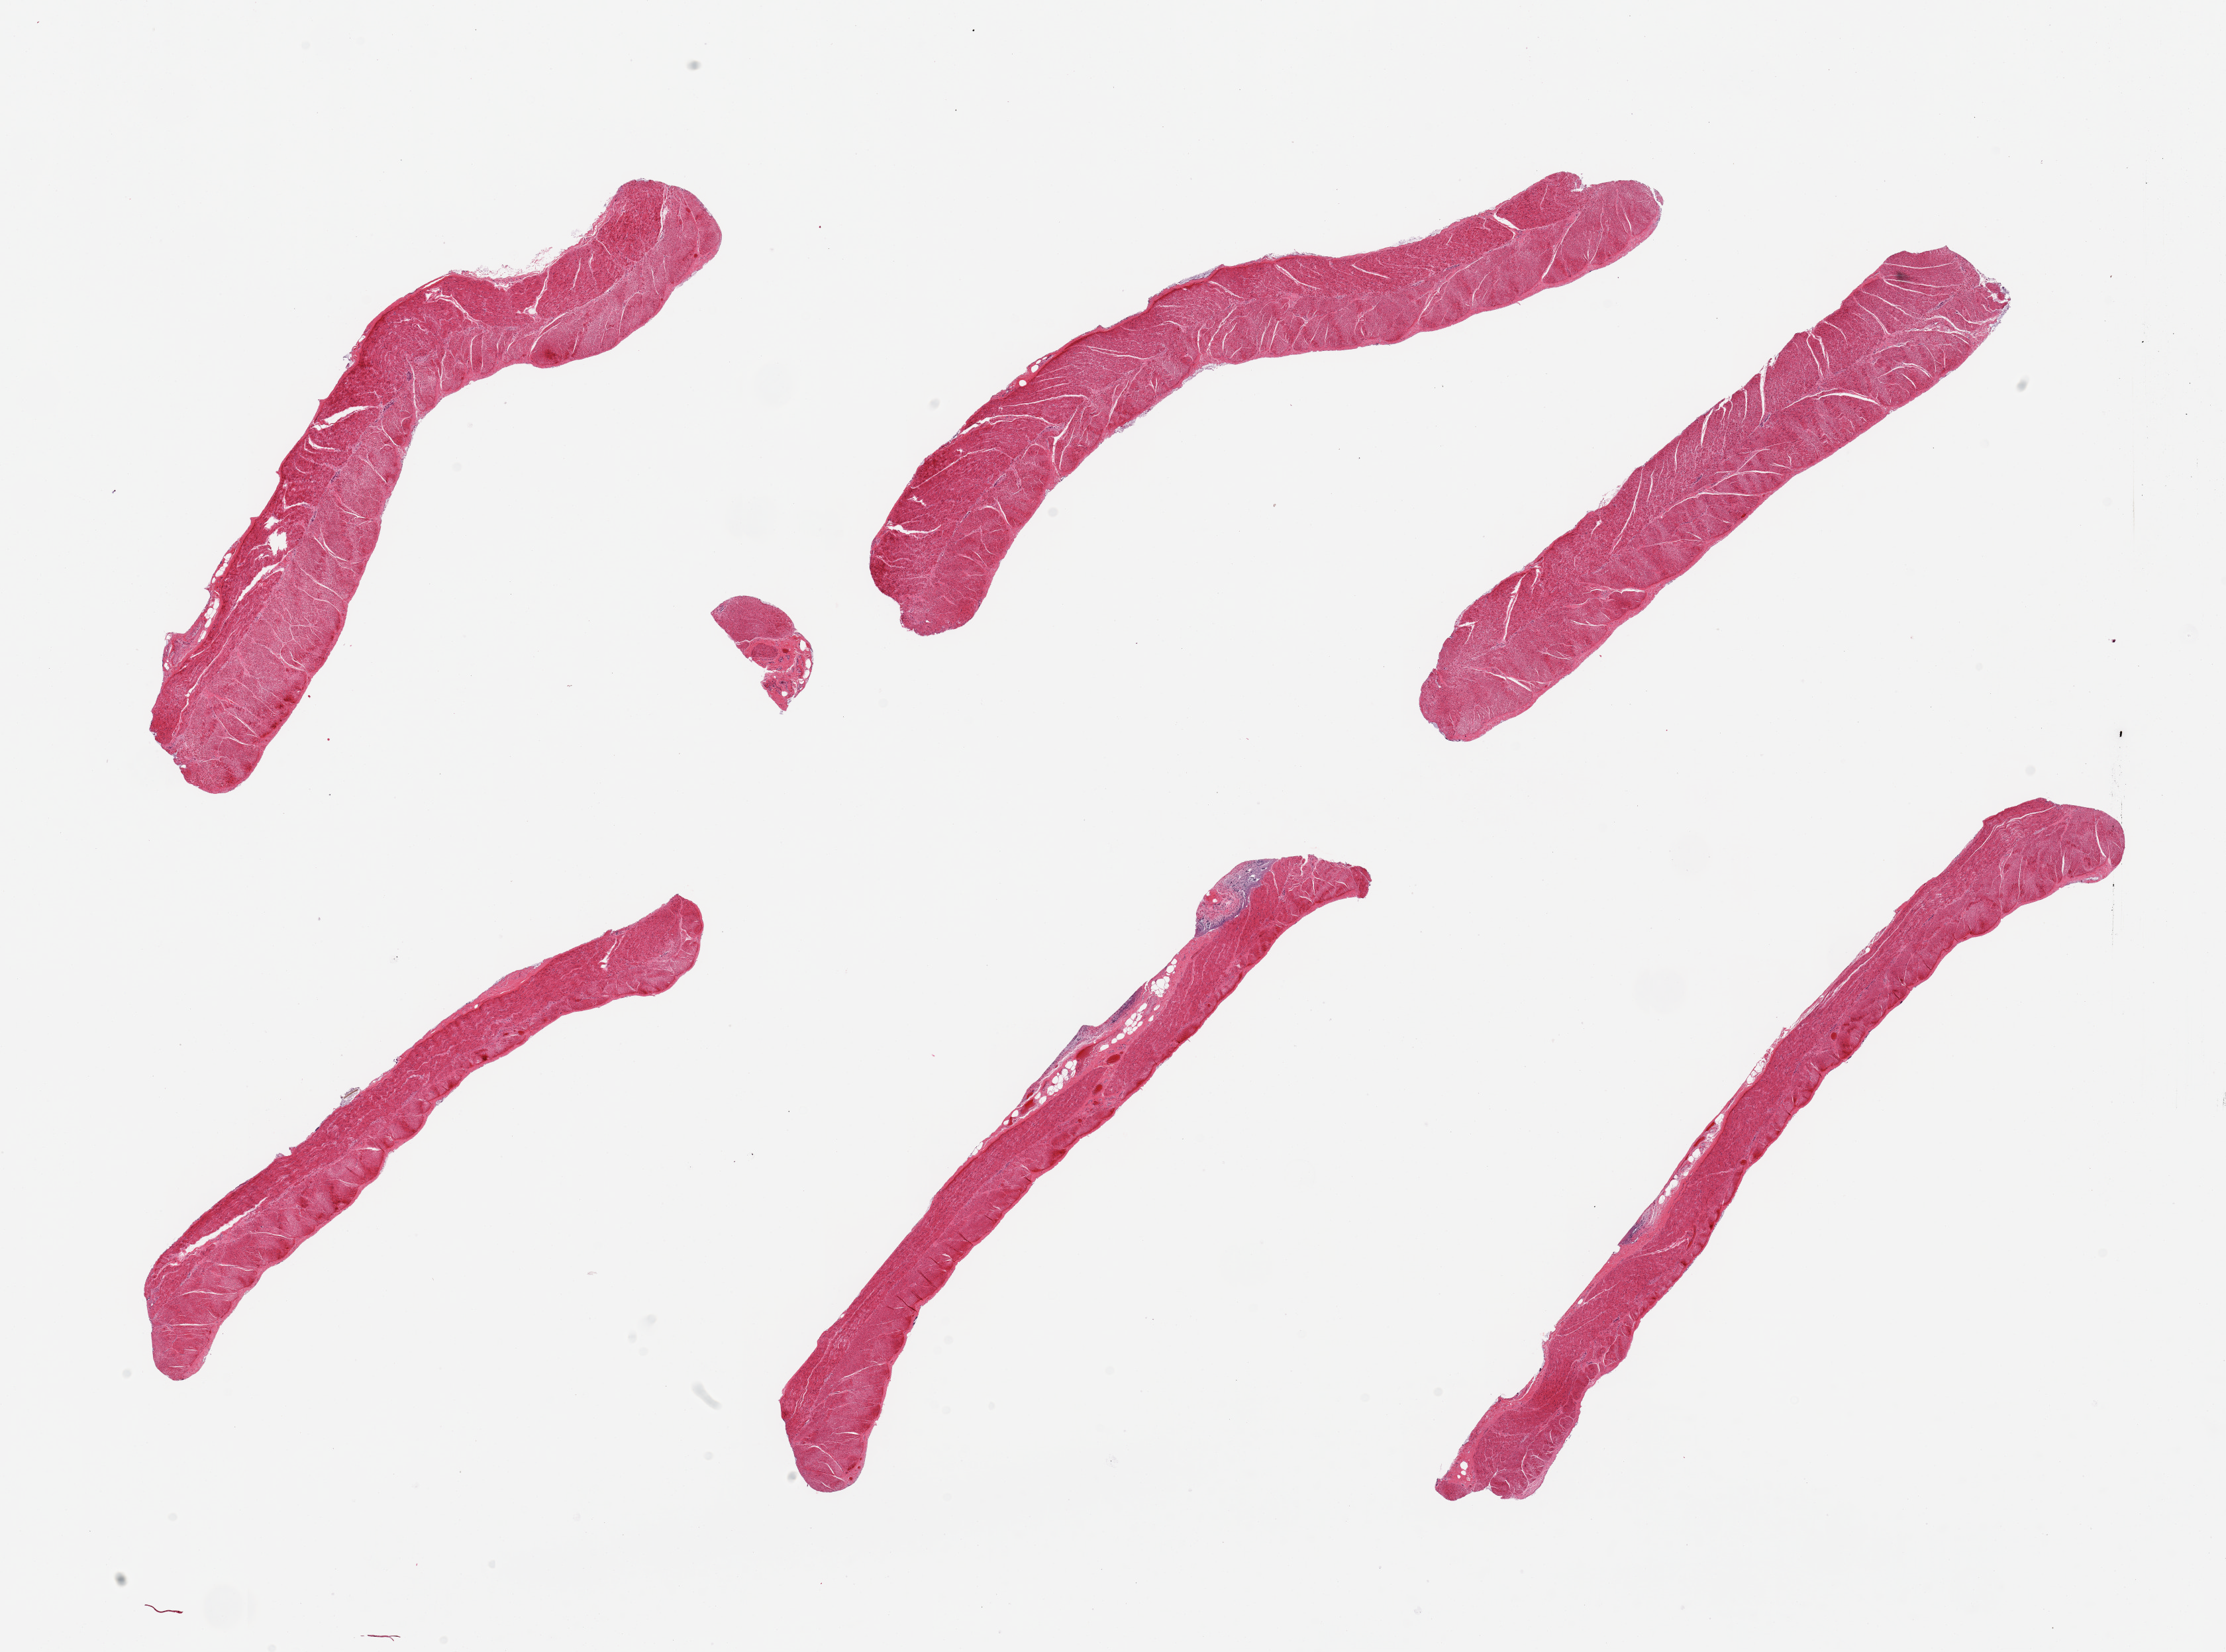
Digitized haematoxylin and eosin-stained section — a low-resolution overview of the entire scanned area, about 26.6 x 19.7 mm (slide scanned at 20x), PAXgene-fixed, paraffin-embedded tissue, section of sigmoid colon (target tissue), donor tissue sample. Donor sex: male.
Review note (as recorded): 6 pieces; predominantly muscularis, two sections include small portion of autolyzed mucosa.